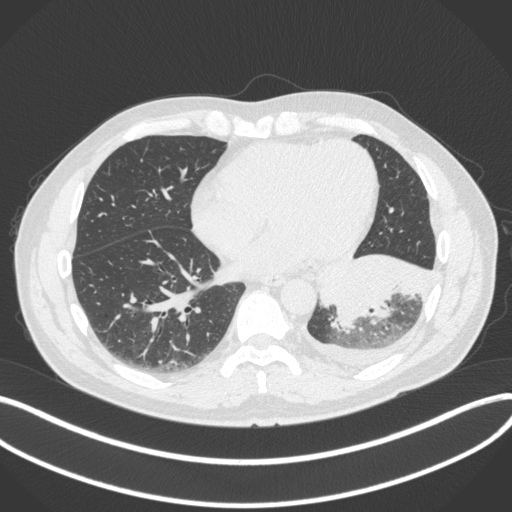
Chest CT, one axial slice. Position 127 of 350 along the scan axis. Reconstruction kernel B31f. 120 kVp. Lung window (W 1500 / L -600 HU). 1 mm slice thickness. 512 × 512 image matrix, field of view 400 × 400 mm. Patient: male, 58 years. Case-level facts recorded for this patient, not image findings: clinical TNM (as recorded): T3 N1 M1b; histopathological grade: G3.
Annotated regions visible in this slice (bounding box drawn by a radiologist):
- lung tumour (recorded histology: small cell carcinoma): bounding box <323,249,437,333> (left, top, right, bottom; pixels)